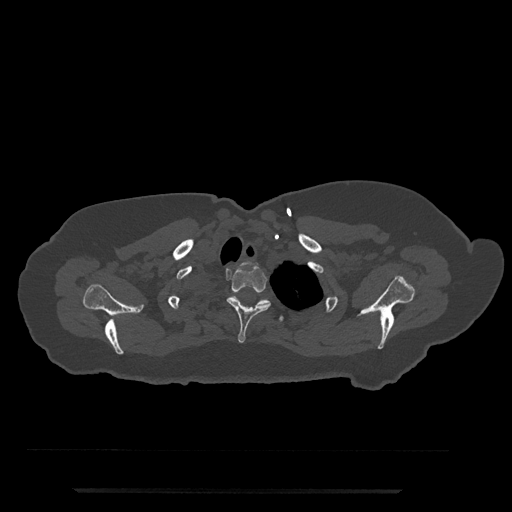
CT including the spine, one axial slice; position 667 of 797 along the scan axis; 120 kVp; bone window (W 1800 / L 400 HU); 512 × 512 image matrix. Female patient, age 51 years. From the clinical record (not read from this slice): primary cancer: neuro.
Annotated regions visible in this slice (semi-automatically segmented with operator editing):
- T1 vertebra: bounding box <244,262,250,264> (left, top, right, bottom; pixels)
- T2 vertebra: <227,266,271,343>
- T3 vertebra: <232,295,284,322>